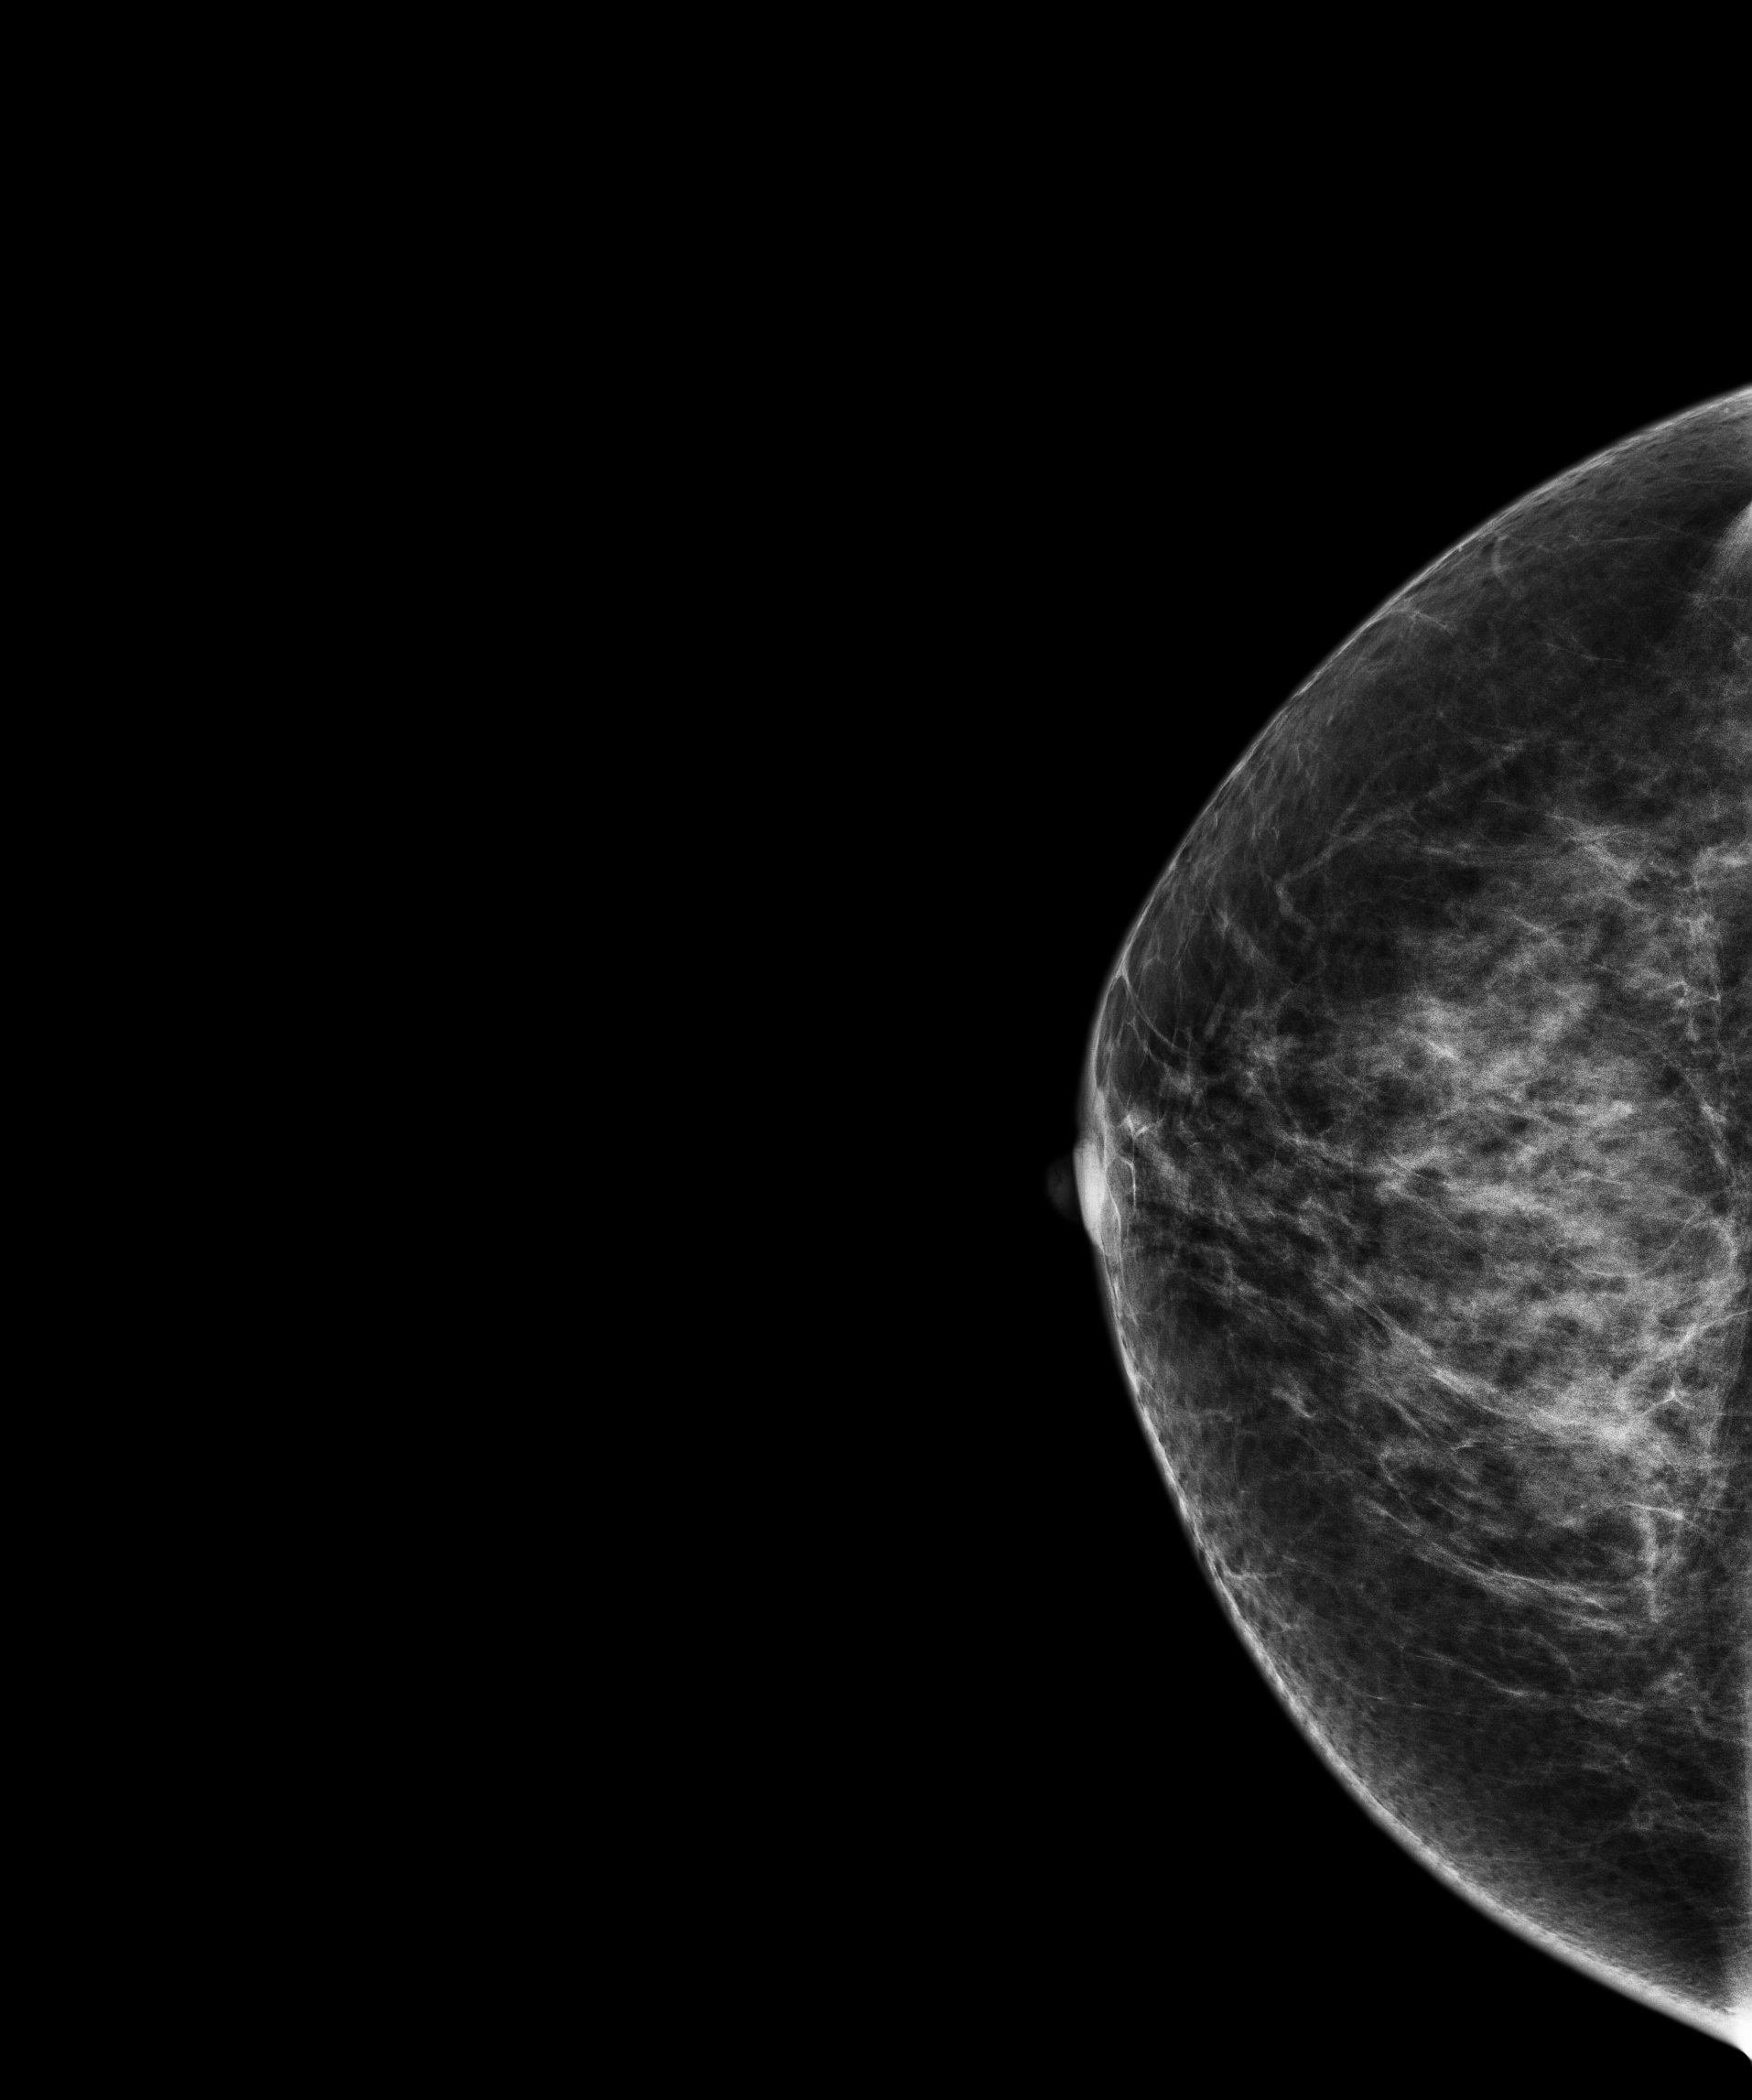
Digital mammogram (FFDM), right breast, CC view, screening examination. Female patient, age 48 years.
Final BI-RADS category for the screening round (tomosynthesis exam, both breasts): category 1.